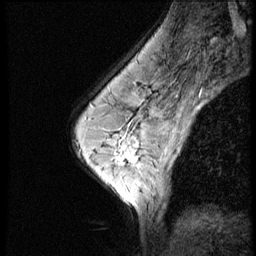
Breast MRI (dynamic contrast-enhanced), one sagittal slice. Slice 36 of 52 in the series (ordered by position). 3 images stored at this slice position (order not interpretable as contrast timing). 1.5 T. TE 4.2 ms, TR 9 ms. 2.5 mm slice thickness. 256 × 256 image matrix. Patient: female, 50 years. Case-level facts recorded for this patient, not image findings: setting: breast cancer imaged before/during neoadjuvant chemotherapy; receptor status: HR-positive, HER2-negative.
Outlined on this slice (semi-automatically segmented with operator editing):
- analysis volume of interest (the breast-tissue region the enhancement analysis was run in; not a lesion): bounding box (x1, y1, x2, y2) in pixels: (103, 130, 151, 181)
- tumour enhancement mask (voxels above the 140 % enhancement threshold inside the analysis volume of interest): (124, 146, 131, 157)